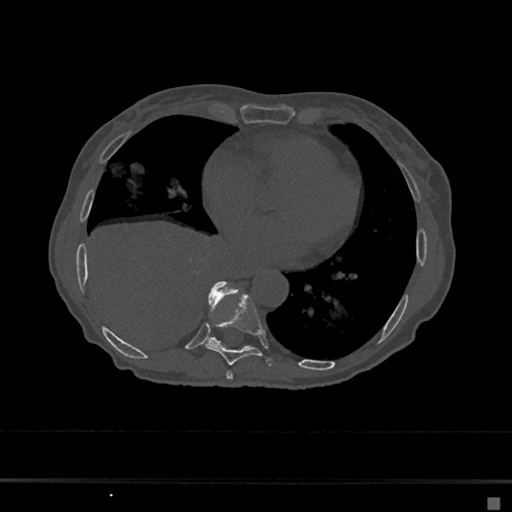
CT including the spine, one axial slice. Position 310 of 797 along the scan axis. Reconstruction kernel Br40s/3. Bone window (W 1800 / L 400 HU). 0.5 mm slice thickness. 512 × 512 image matrix, field of view 360 × 360 mm. Female patient, age 68 years. Case-level facts recorded for this patient, not image findings: primary cancer: renal.
Structures marked on this image (semi-automatic segmentation, software-assisted and operator-edited):
- T7 vertebra: bounding box <226,371,233,380> (left, top, right, bottom; pixels)
- T8 vertebra: <205,293,273,367>
- T9 vertebra: <208,281,238,345>